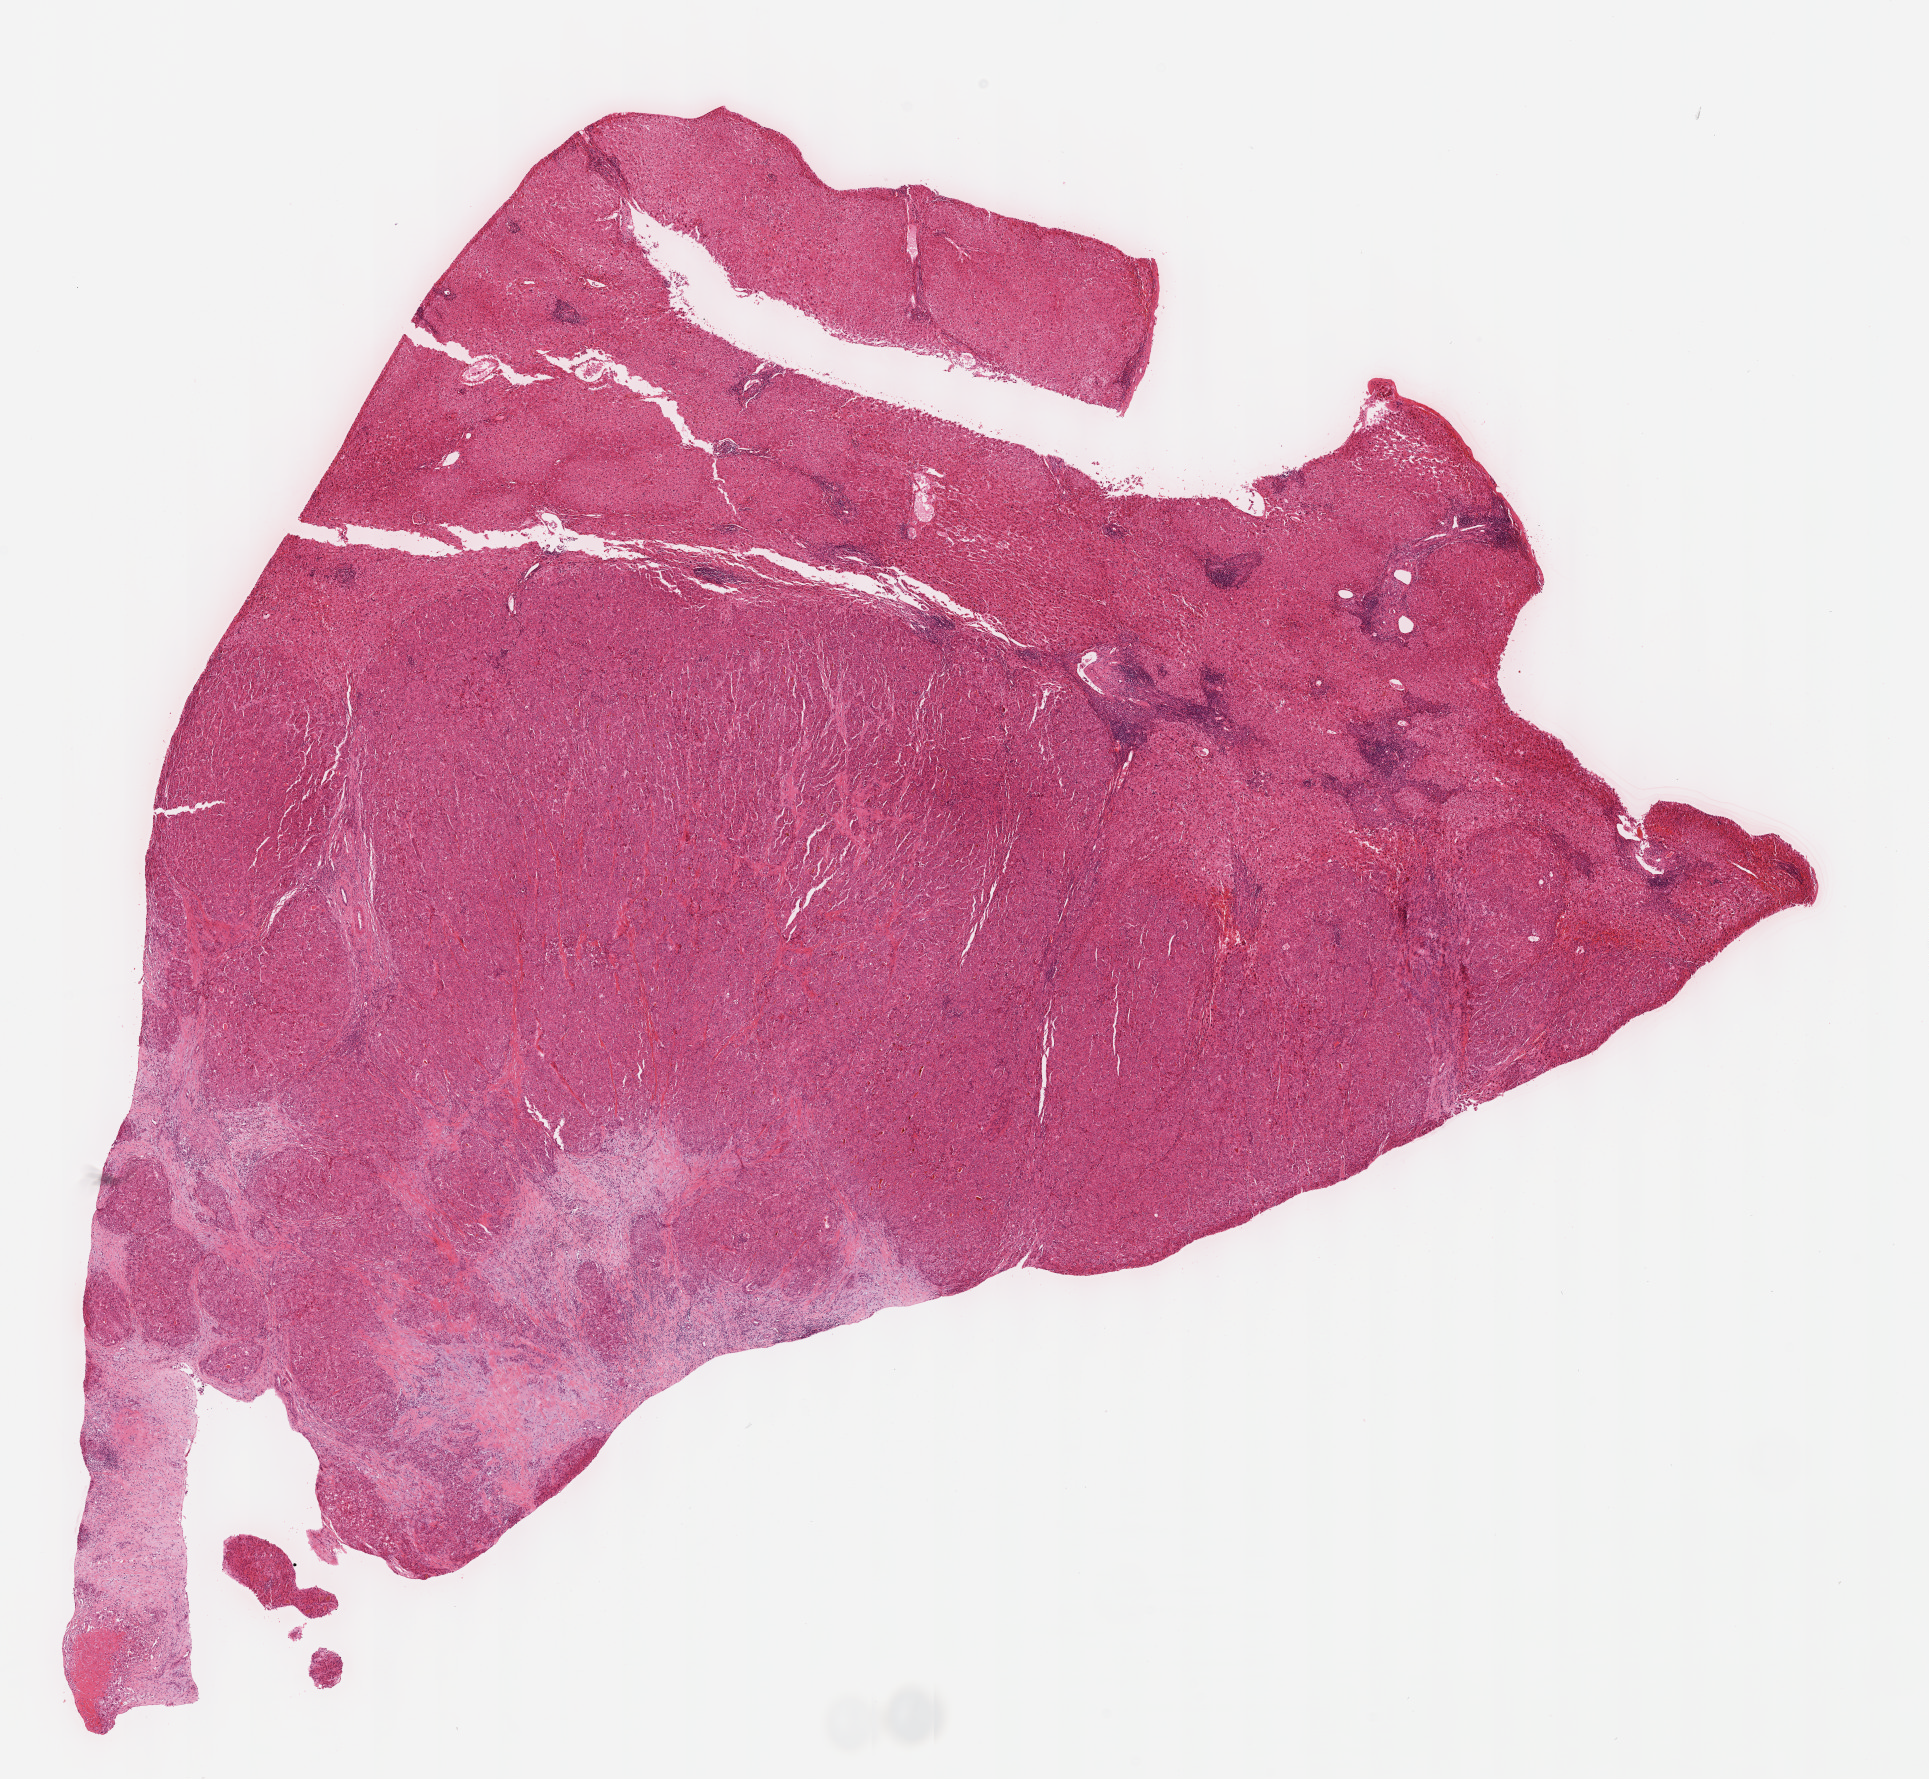
Whole-slide histology image, H&E — shown as a low-resolution overview of the whole scanned area (about 15.6 x 14.4 mm). Formalin-fixed paraffin-embedded (FFPE) diagnostic section. Primary tumour sample from the liver. Male patient; age at initial diagnosis 66 years. Histologic grade: G2 (moderately differentiated).
Histologic diagnosis: Hepatocellular carcinoma, NOS. AJCC pathologic stage: I (7th edition).